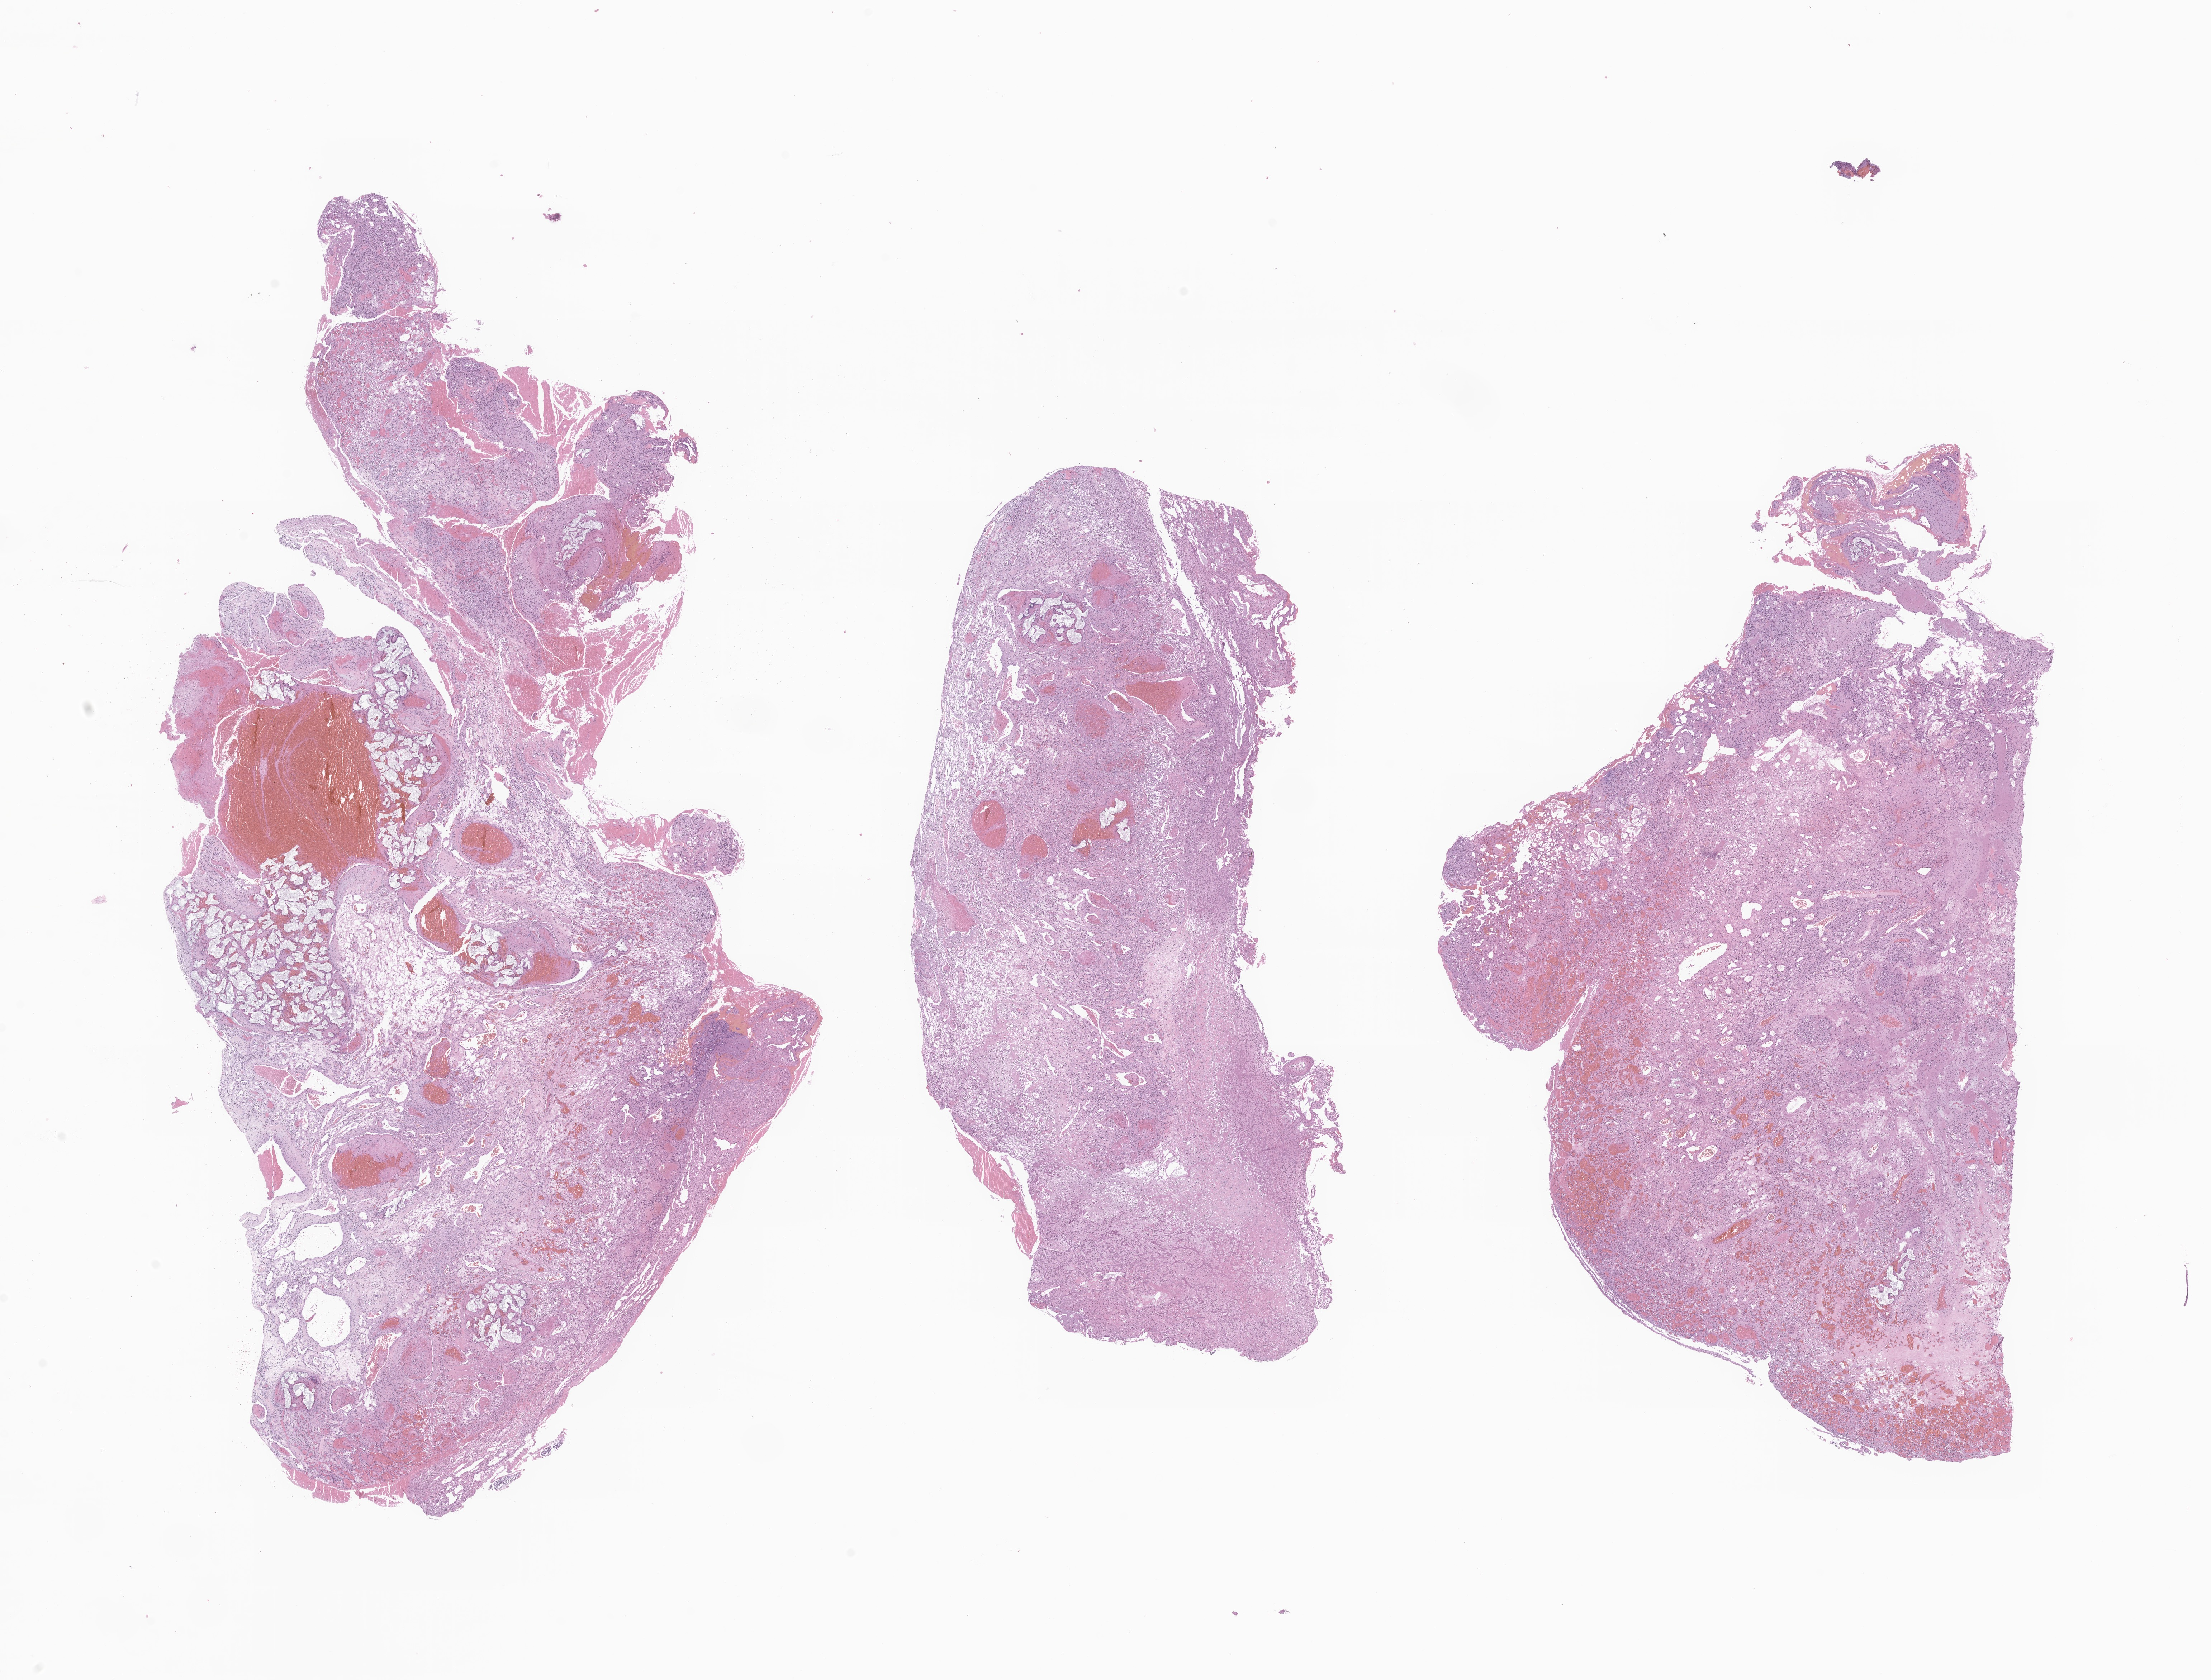
Digitized hematoxylin and eosin (H&E)-stained section of tumor tissue from the brain — whole scanned area (about 26.0 x 19.8 mm) shown as a low-resolution overview. Formalin-fixed, paraffin-embedded (FFPE) tissue. Patient: female, age 93 months (7 years 9 months).
Diagnosis (ICD-O-3 morphology term): Malignant tumor, spindle cell type.